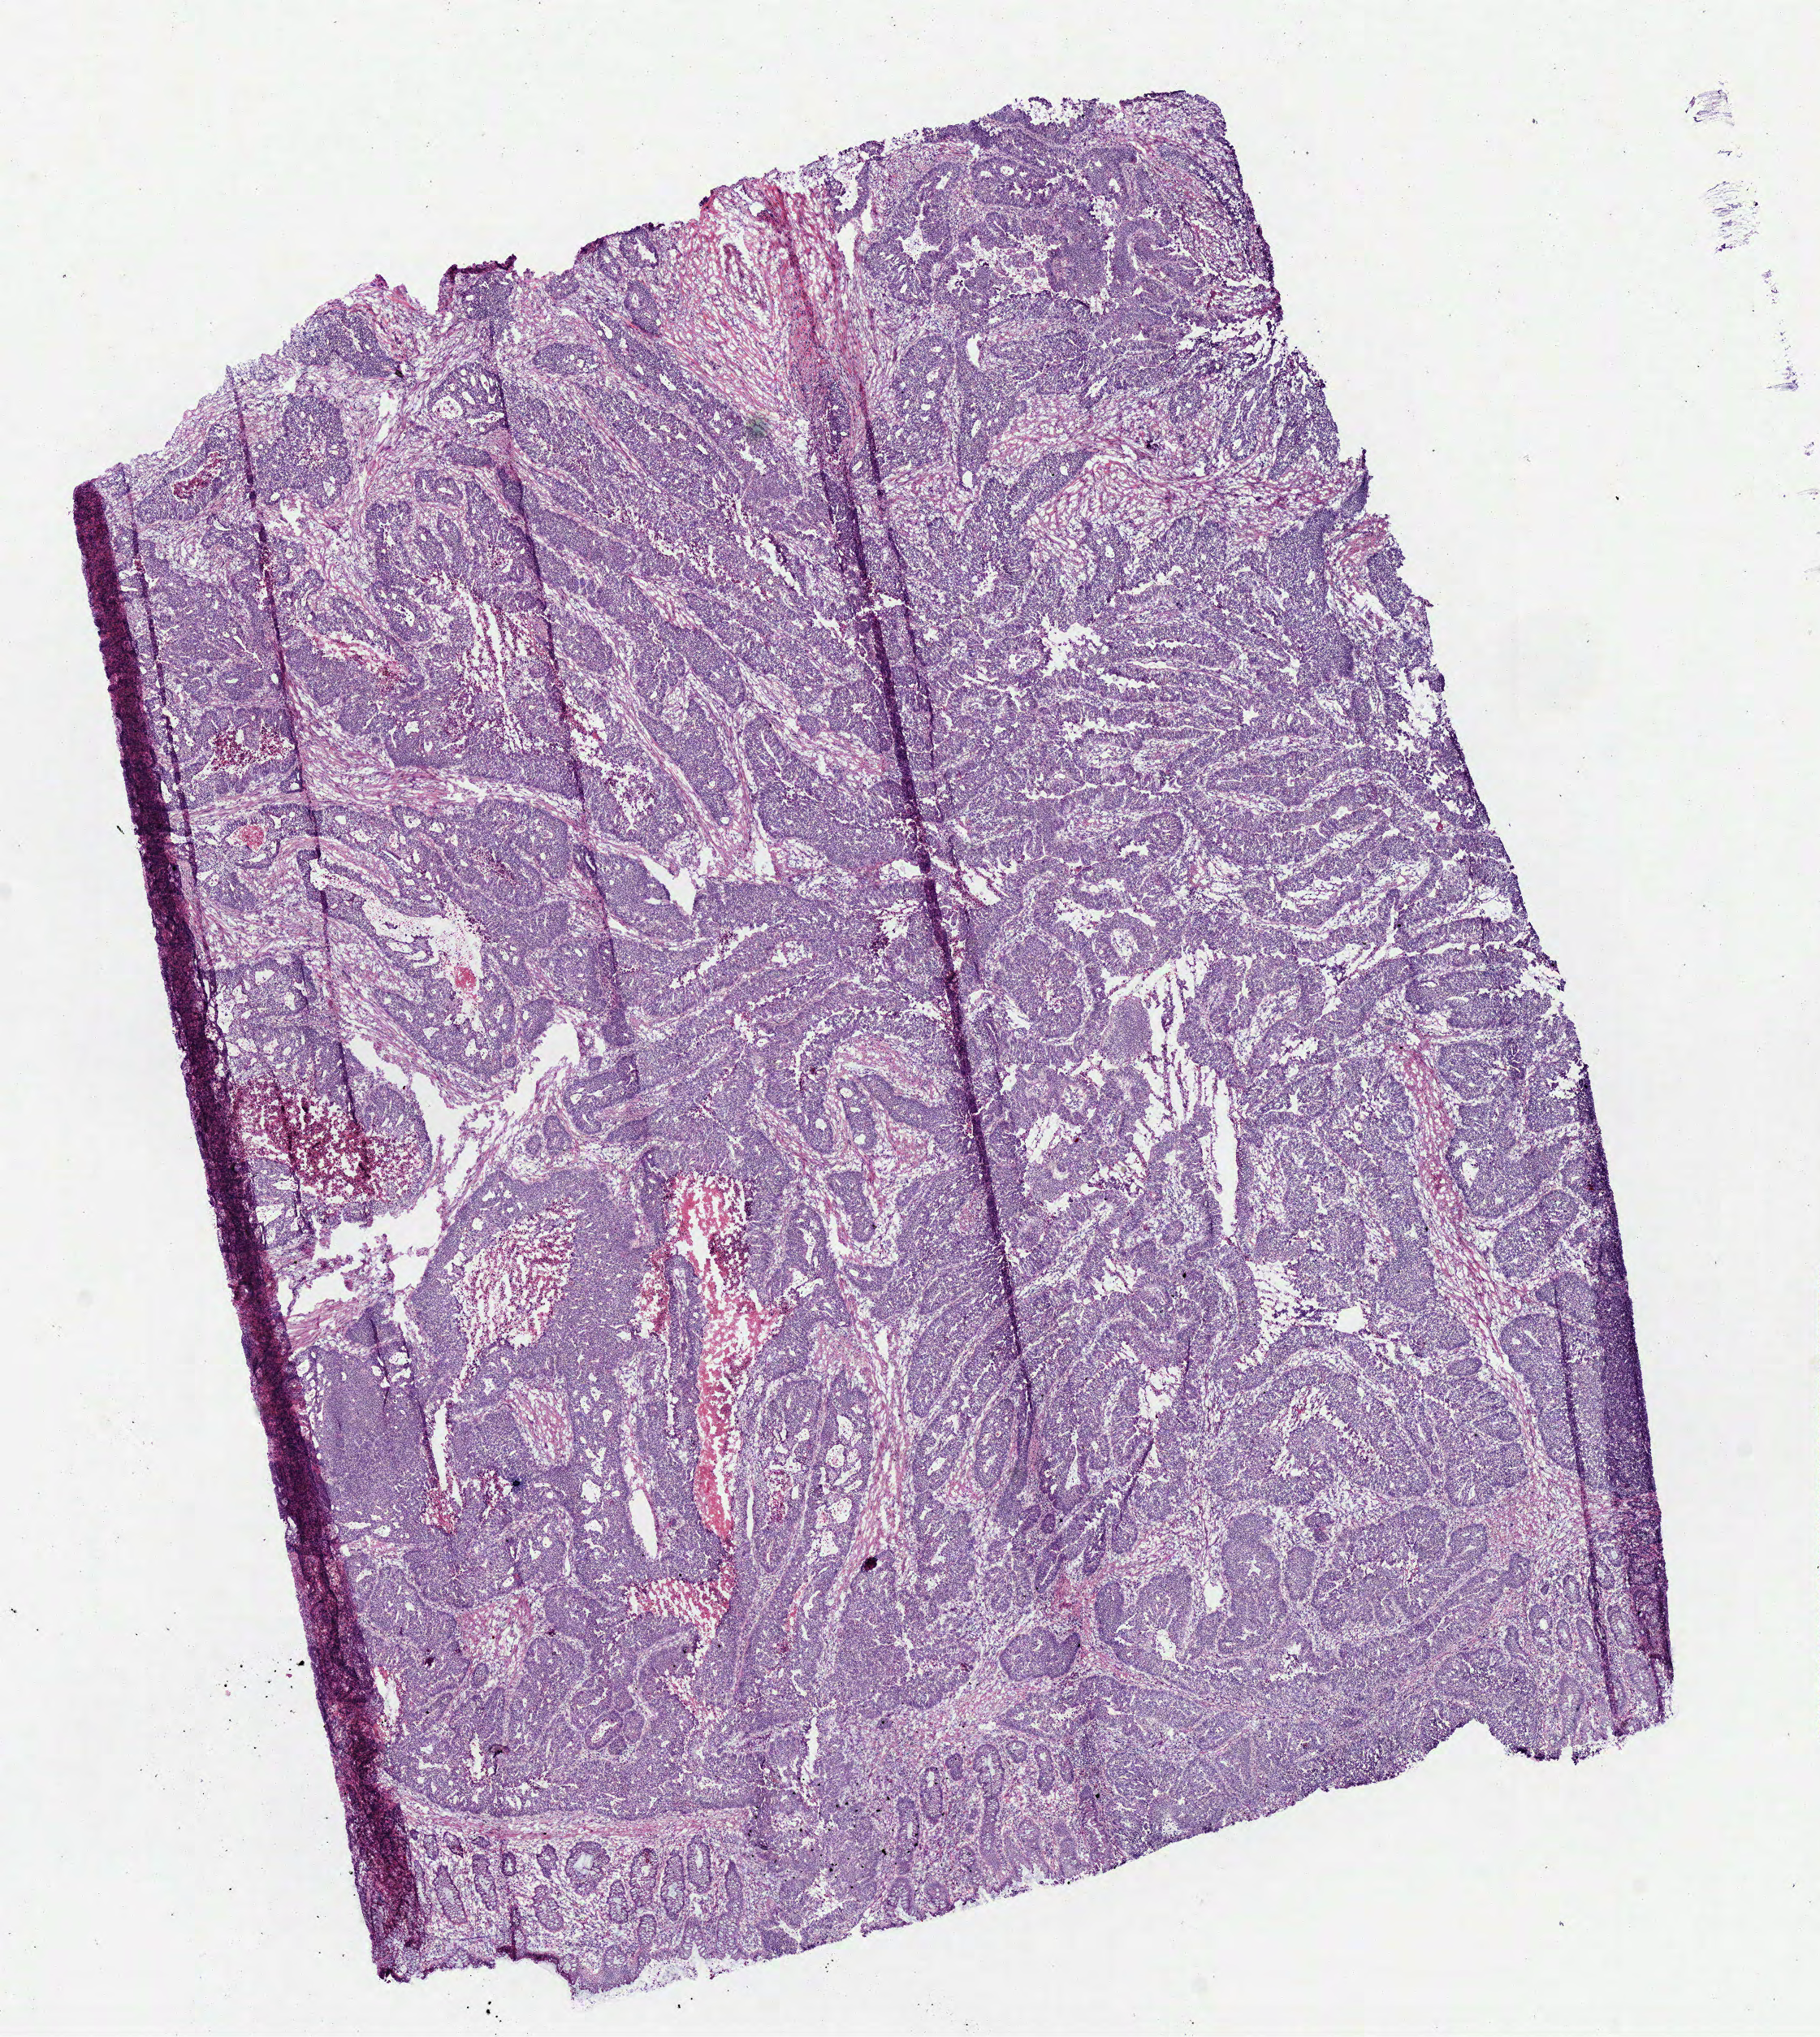
Whole-slide histology image, H&E-stained, a low-resolution overview of the entire scanned area, about 8.8 x 9.9 mm, frozen section from the bottom of the tissue portion, primary tumour sample from the rectum. Female patient; age at initial diagnosis 48 years. Pathologist review of this section (percent, as recorded): tumour cells 80%, tumour nuclei 80%, normal cells 5%, stromal cells 10%, necrosis 5%.
Lymph nodes positive (case pathology): 1 of 15 examined. AJCC pathologic stage: IIIB (7th edition). Pathologic diagnosis: Adenocarcinoma in tubulovillous adenoma.